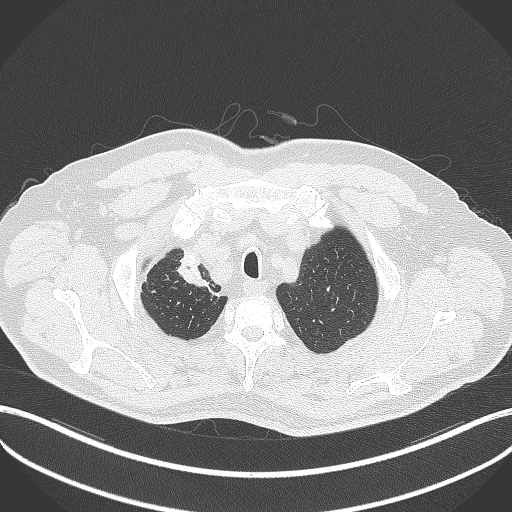
Chest CT, one axial slice; slice 339 of 411 in the series (ordered by position); reconstruction kernel B70f; 120 kVp; lung window (W 1500 / L -600 HU); 1 mm slice thickness; 512 × 512 image matrix. Male patient, age 60 years. Case-level facts recorded for this patient, not image findings: clinical TNM (as recorded): T1b N1 M0.
Annotated regions visible in this slice (rectangle marked by the reading radiologist):
- lung tumour (recorded histology: squamous cell carcinoma): bounding box <175,246,208,289> (left, top, right, bottom; pixels)